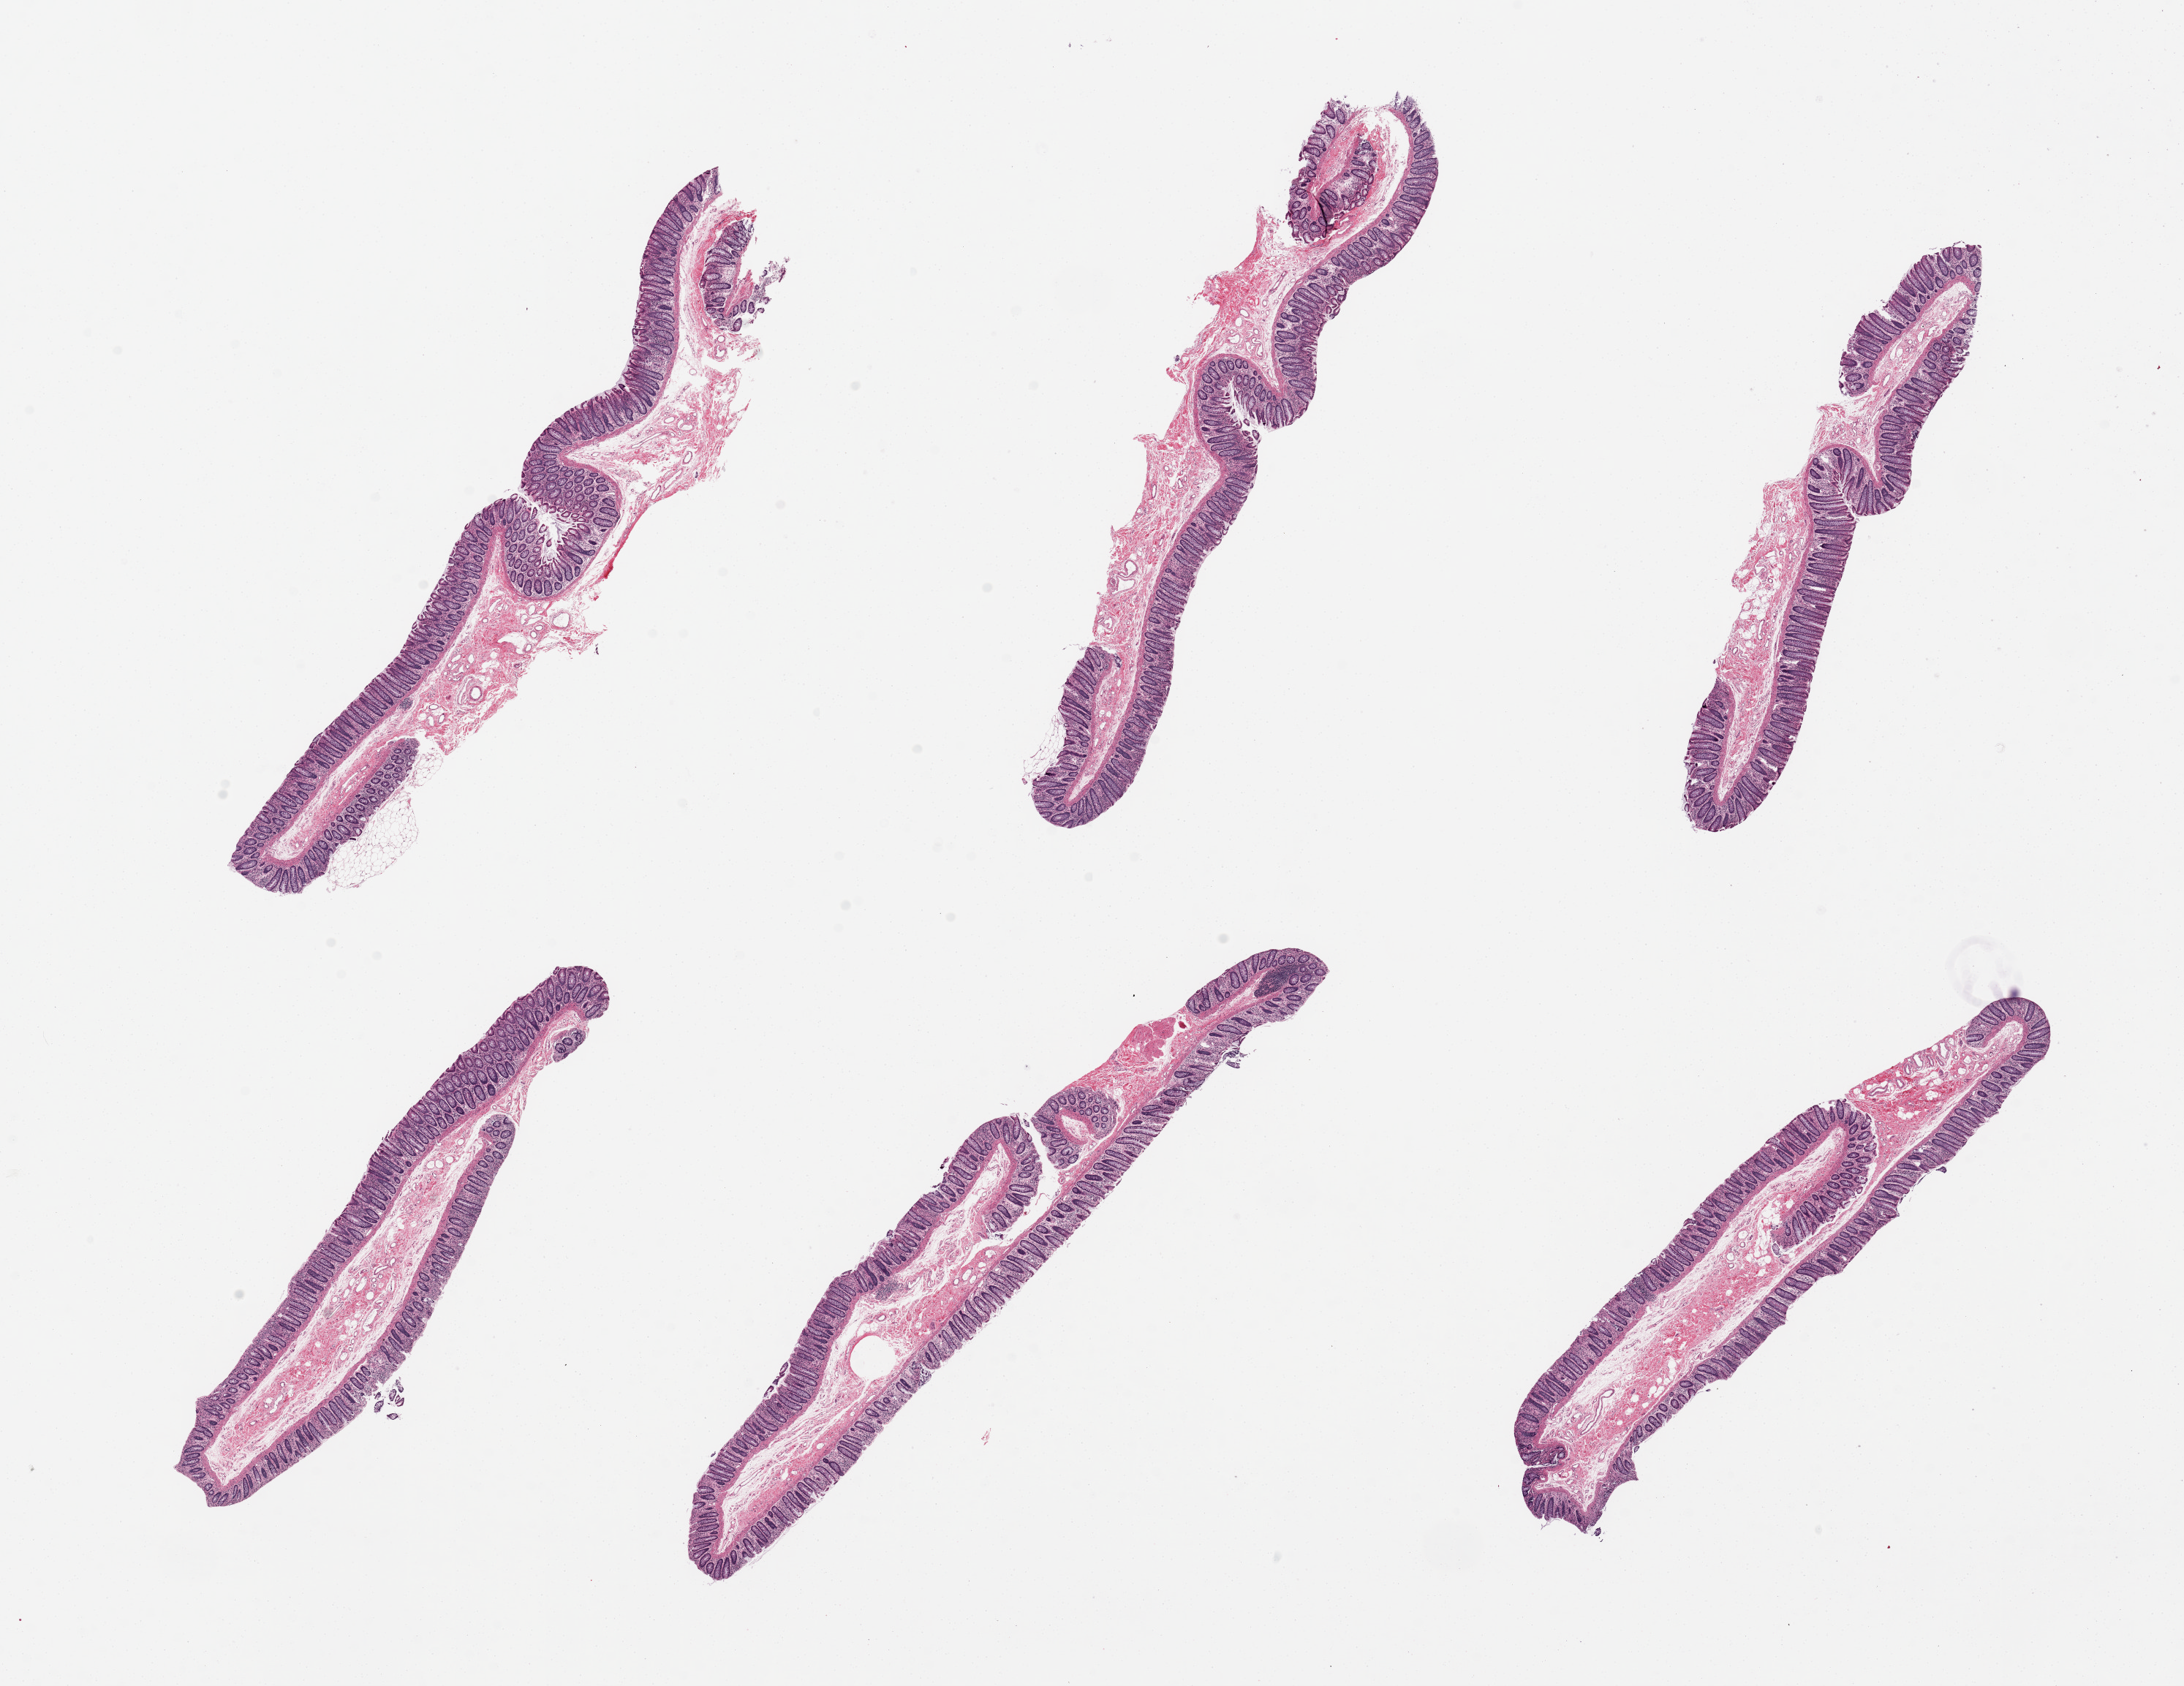
Haematoxylin and eosin whole-slide image, shown as a low-resolution overview of the whole scanned area (about 23.6 x 18.2 mm). PAXgene-fixed paraffin-embedded (PFPE) section. Section of transverse colon (target tissue). Tissue donor sample. Donor sex: female.
Review note (as recorded): 6 pieces, up to 9x2mm; muscosa well preserved, ~30% thickness.